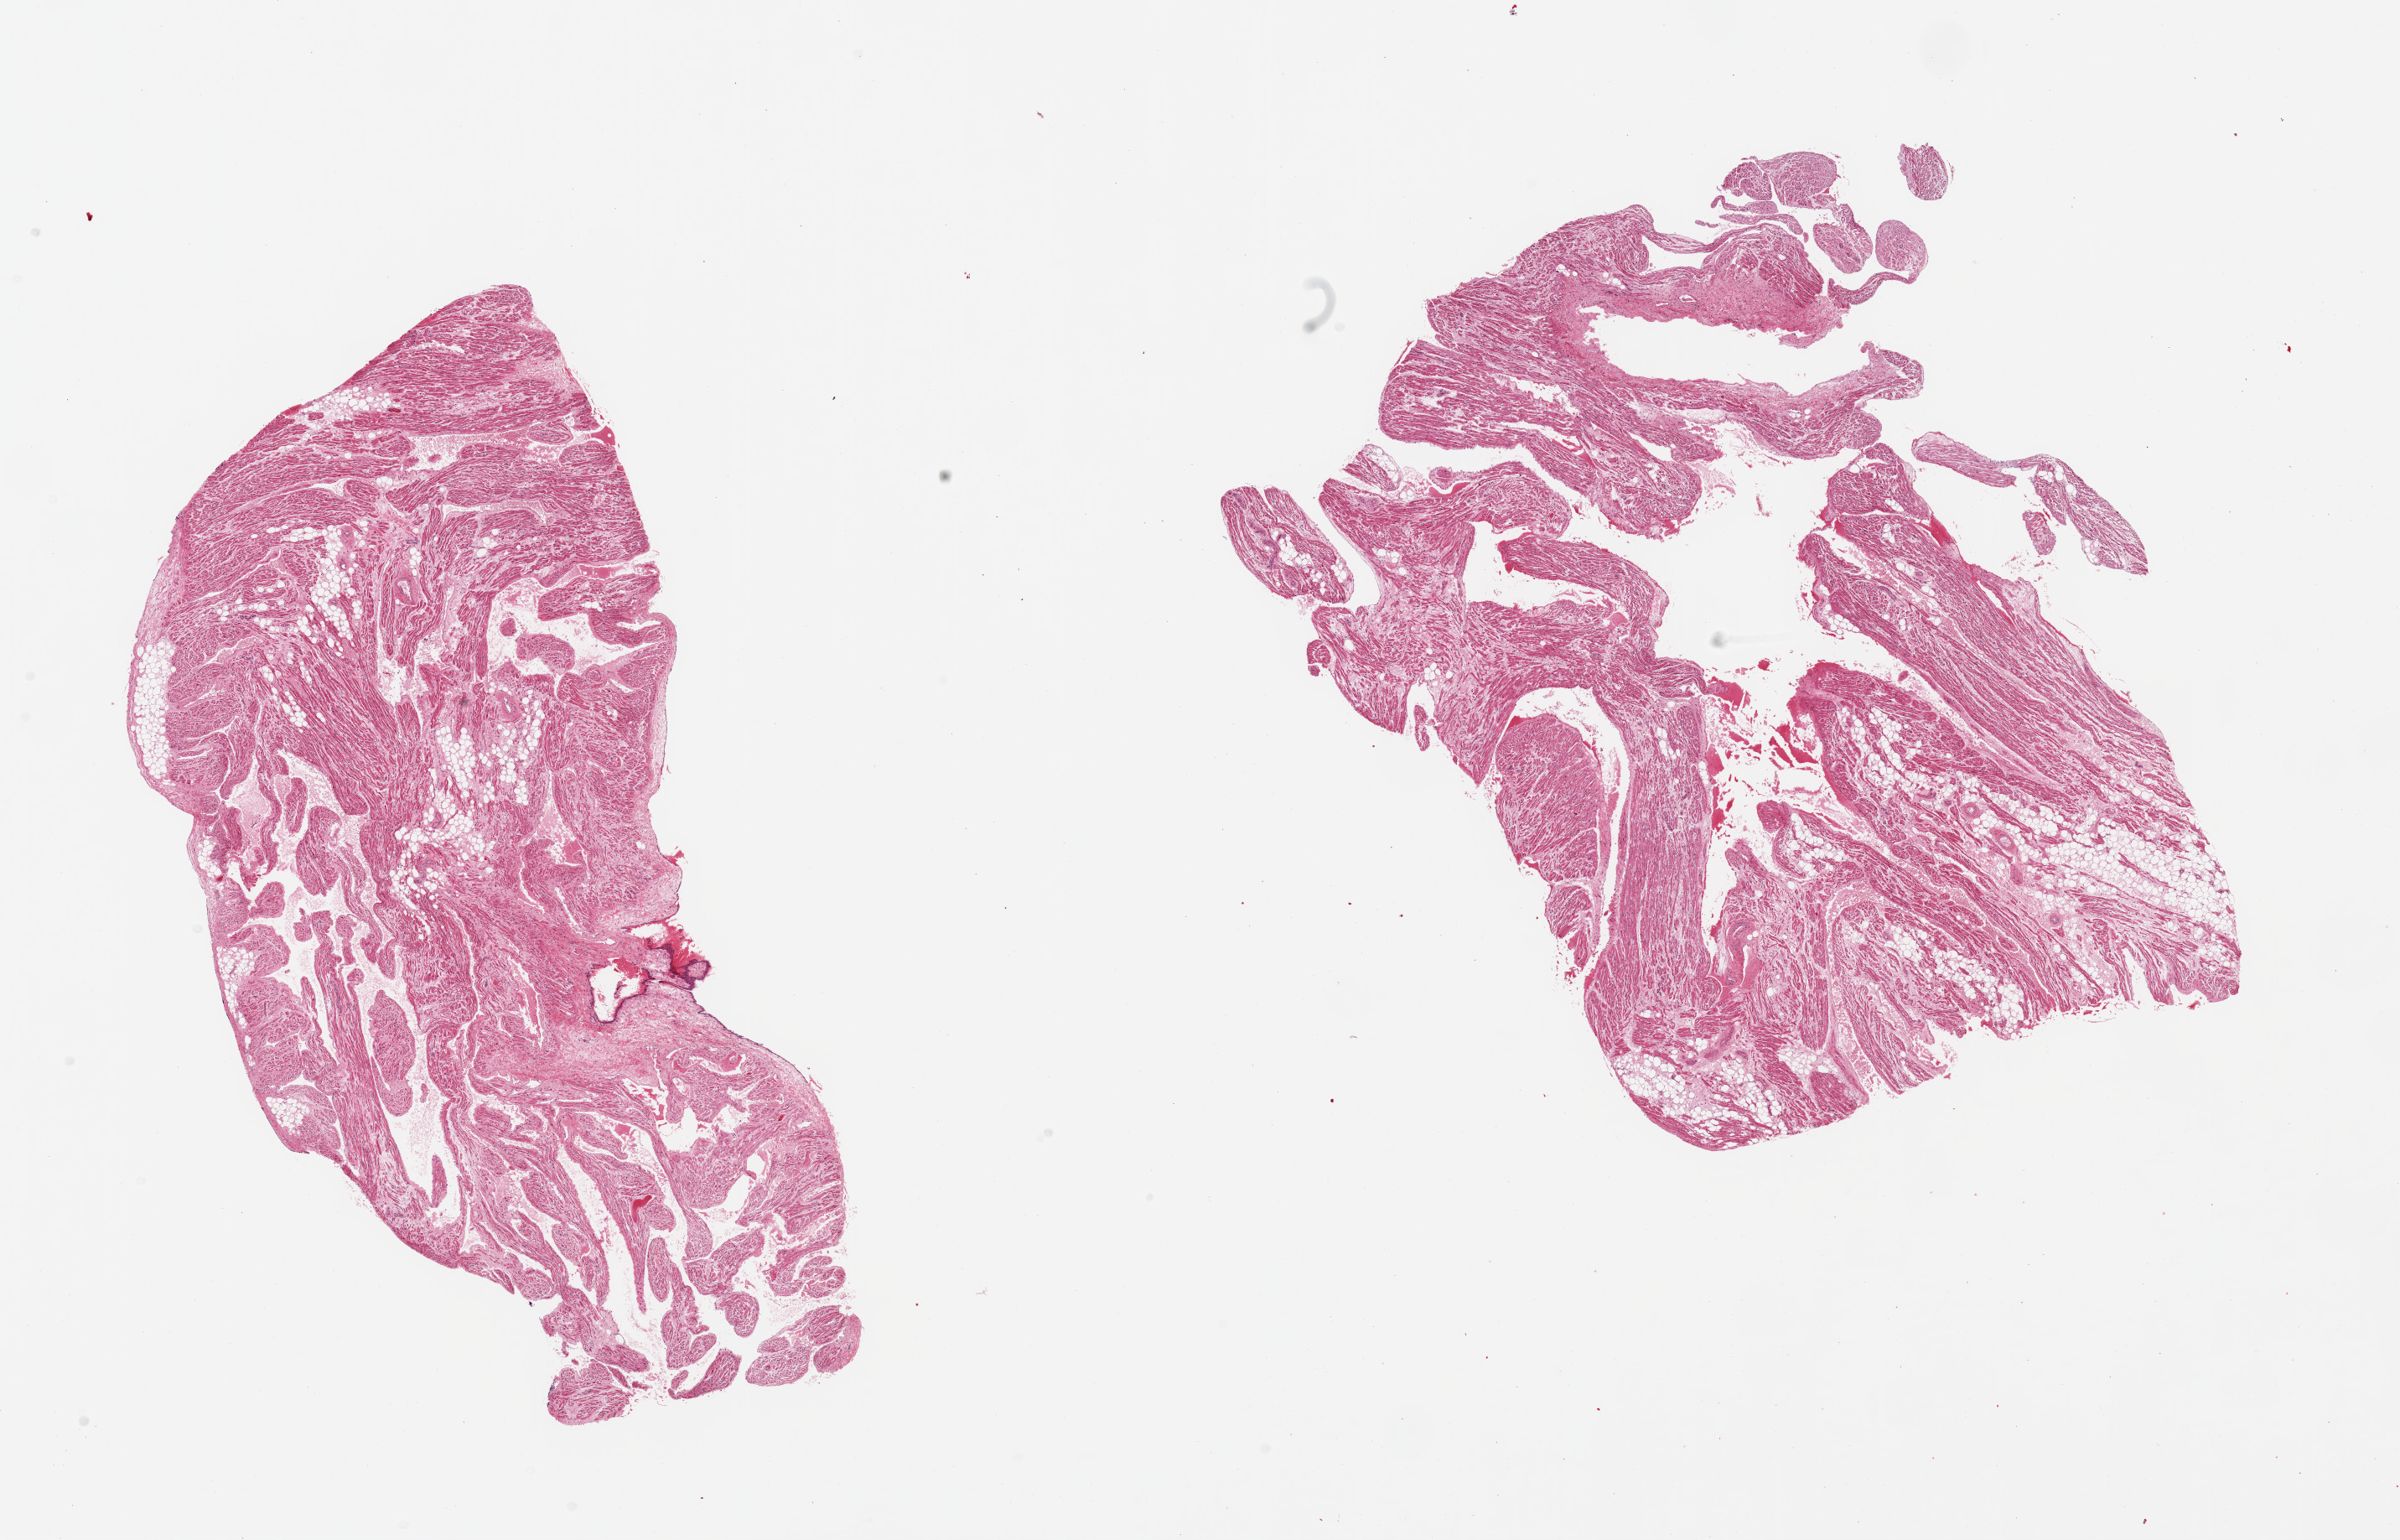
Digitized hematoxylin and eosin (H&E)-stained section, brightfield, low-resolution overview of the scanned area, about 22.6 x 14.5 mm (from a 20x scan). PAXgene-fixed paraffin-embedded (PFPE) section. Section of auricular appendage (target tissue). Donor tissue sample.
Reviewer comment on this tissue sample: 2 pieces; 10% internal fat content.